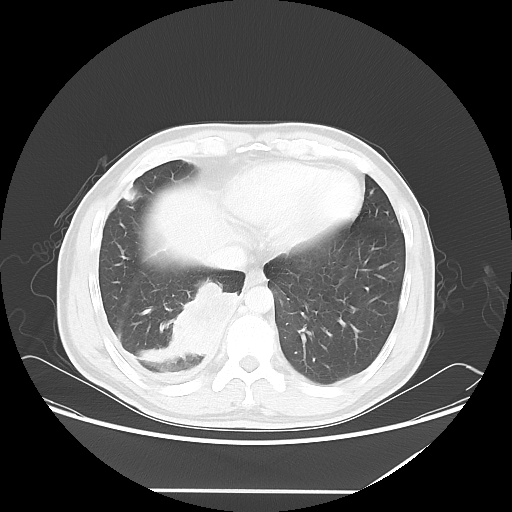
Chest CT, one axial slice. Slice 18 of 60 in the series (ordered by position). Reconstruction kernel LUNG. Lung window (W 1500 / L -600 HU). 5 mm slice thickness. 512 × 512 image matrix. Patient: male, 48 years. Case-level facts recorded for this patient, not image findings: clinical TNM (as recorded): T3 N3 M1a.
Annotated regions visible in this slice (bounding box drawn by a radiologist):
- lung tumour (recorded histology: squamous cell carcinoma): box from (x=171, y=276) to (x=240, y=363) px